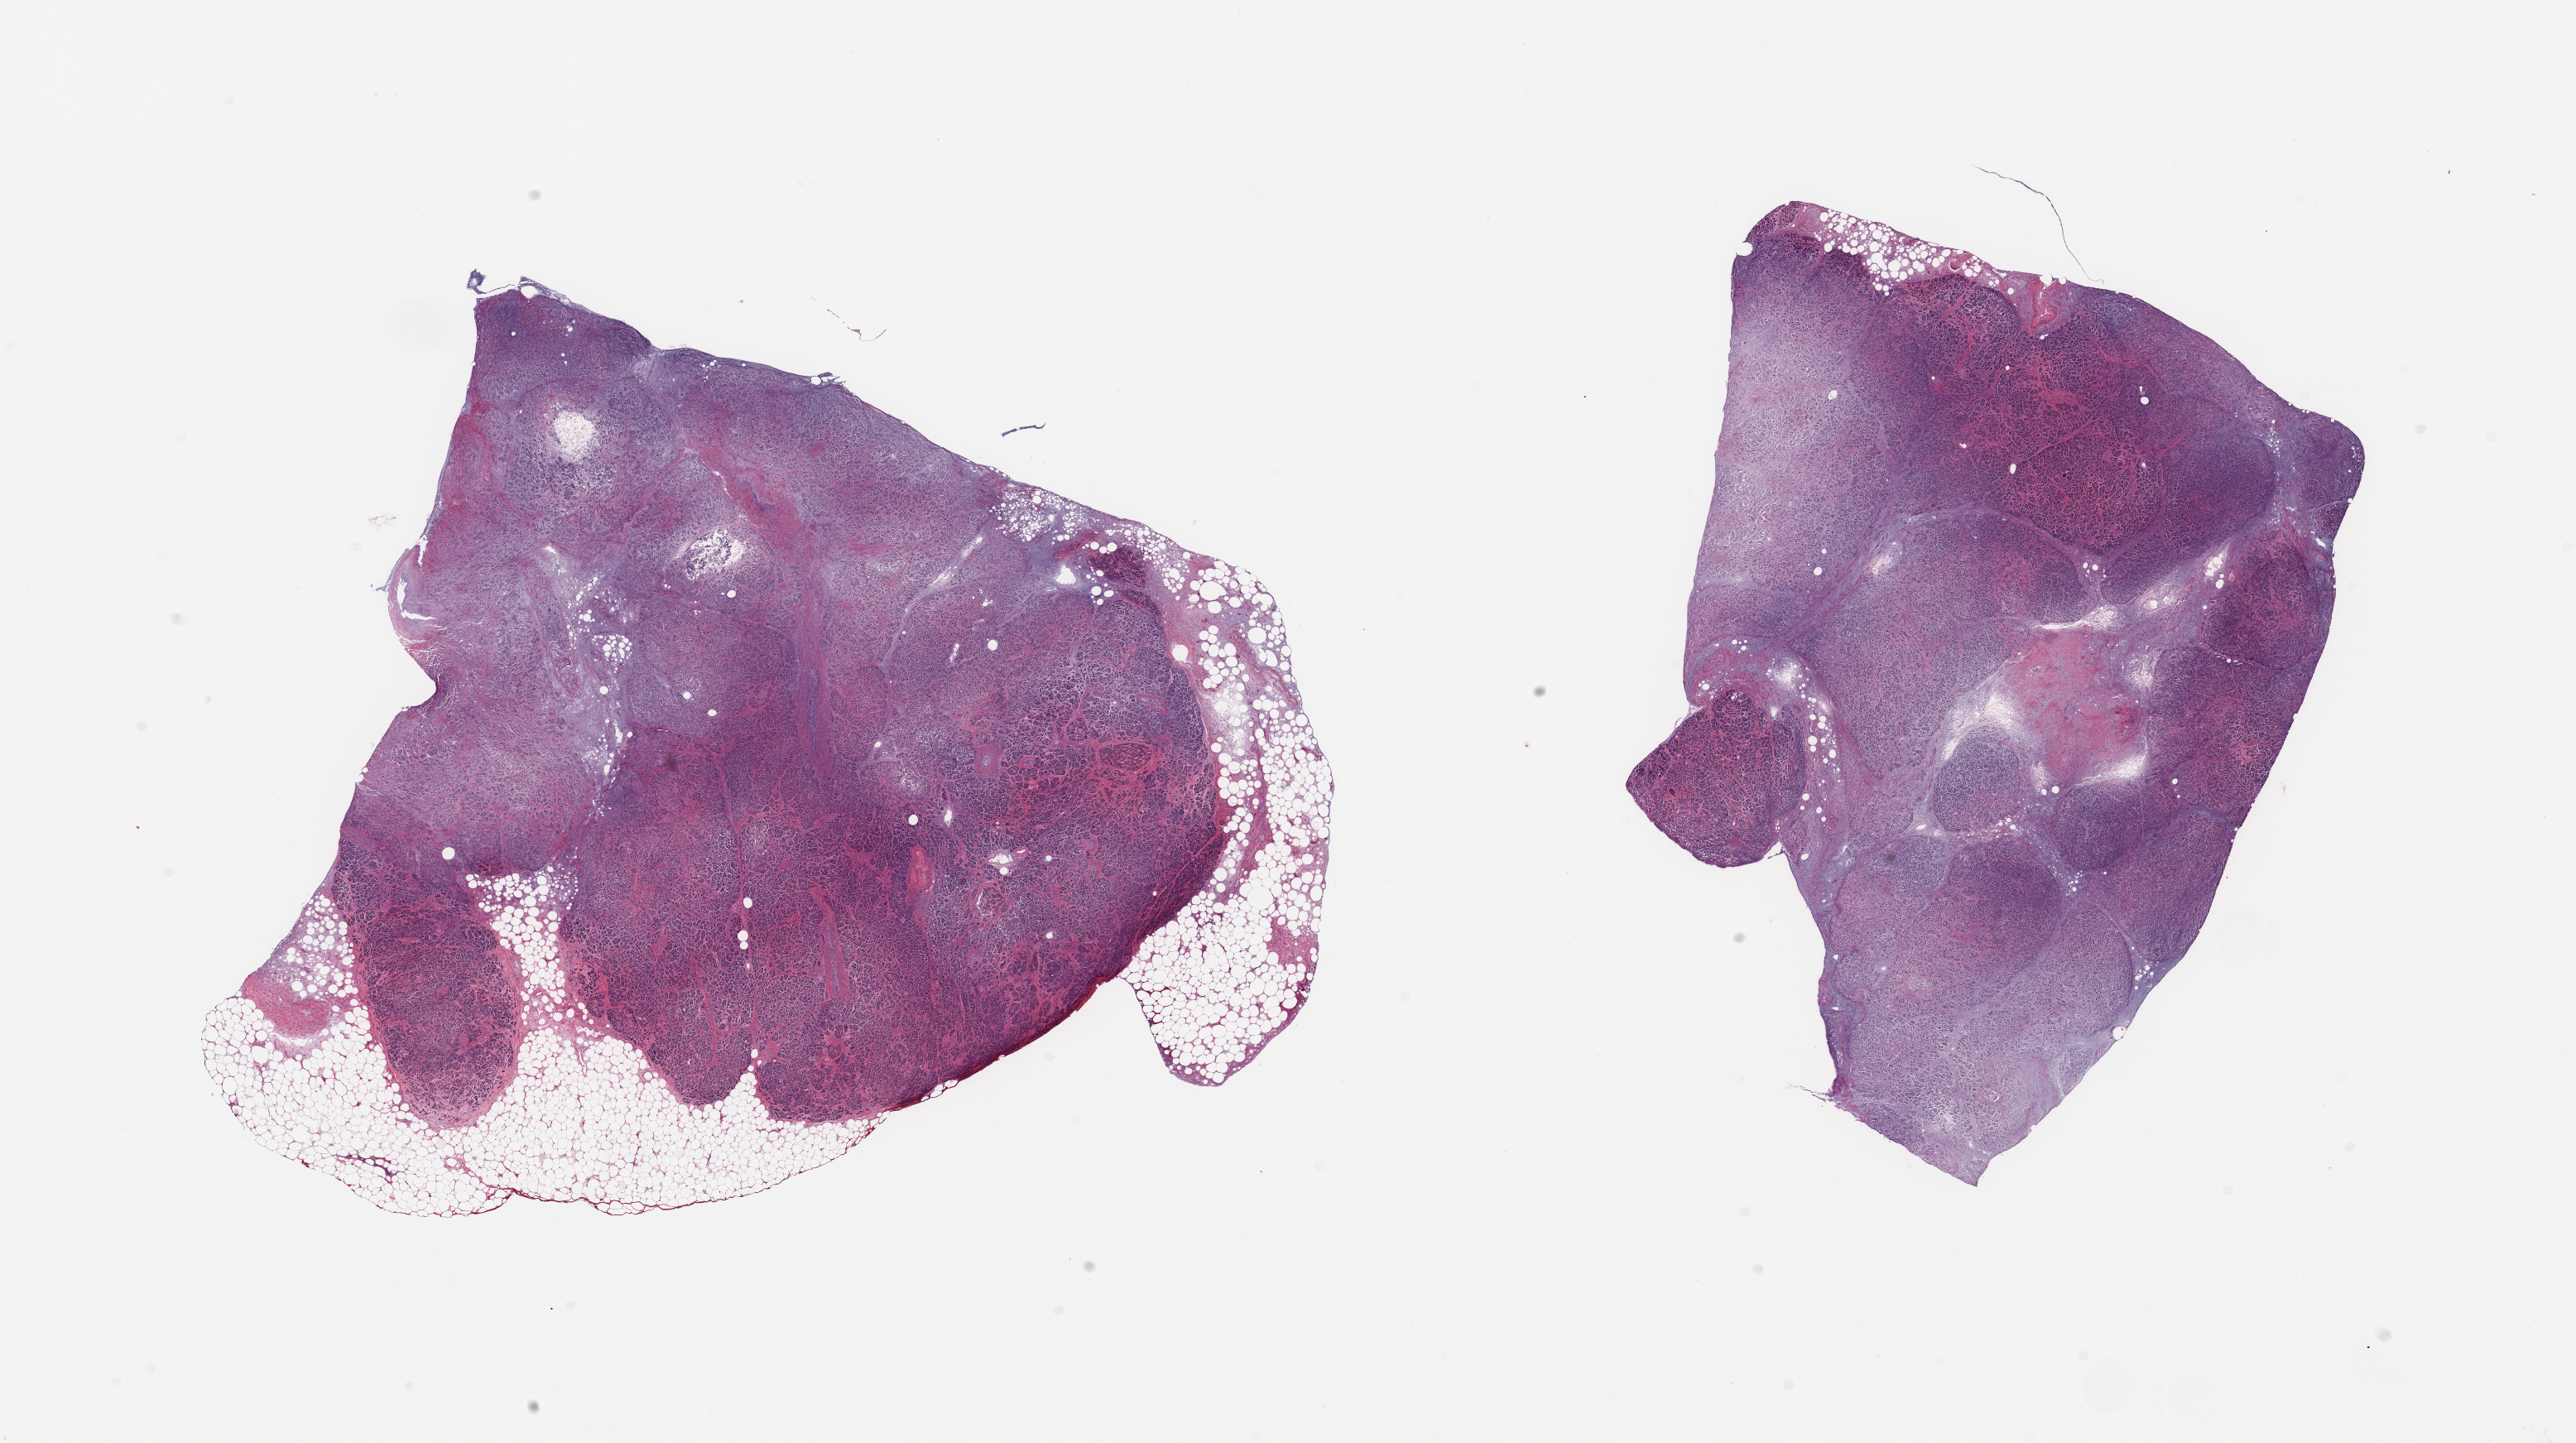
Whole-slide image, H&E stain, whole scanned area (about 24.6 x 13.8 mm, slide scanned at 20x) shown as a low-resolution overview, PAXgene-fixed, paraffin-embedded tissue, sampled site (target tissue): pancreas, donor tissue sample. Donor sex: male.
* reviewer comment on this tissue sample: 2 pieces; moderate to severe parenchymal and fat autolysis, ~15% and 5% external fat, interstitial fibrosis, very rare islets